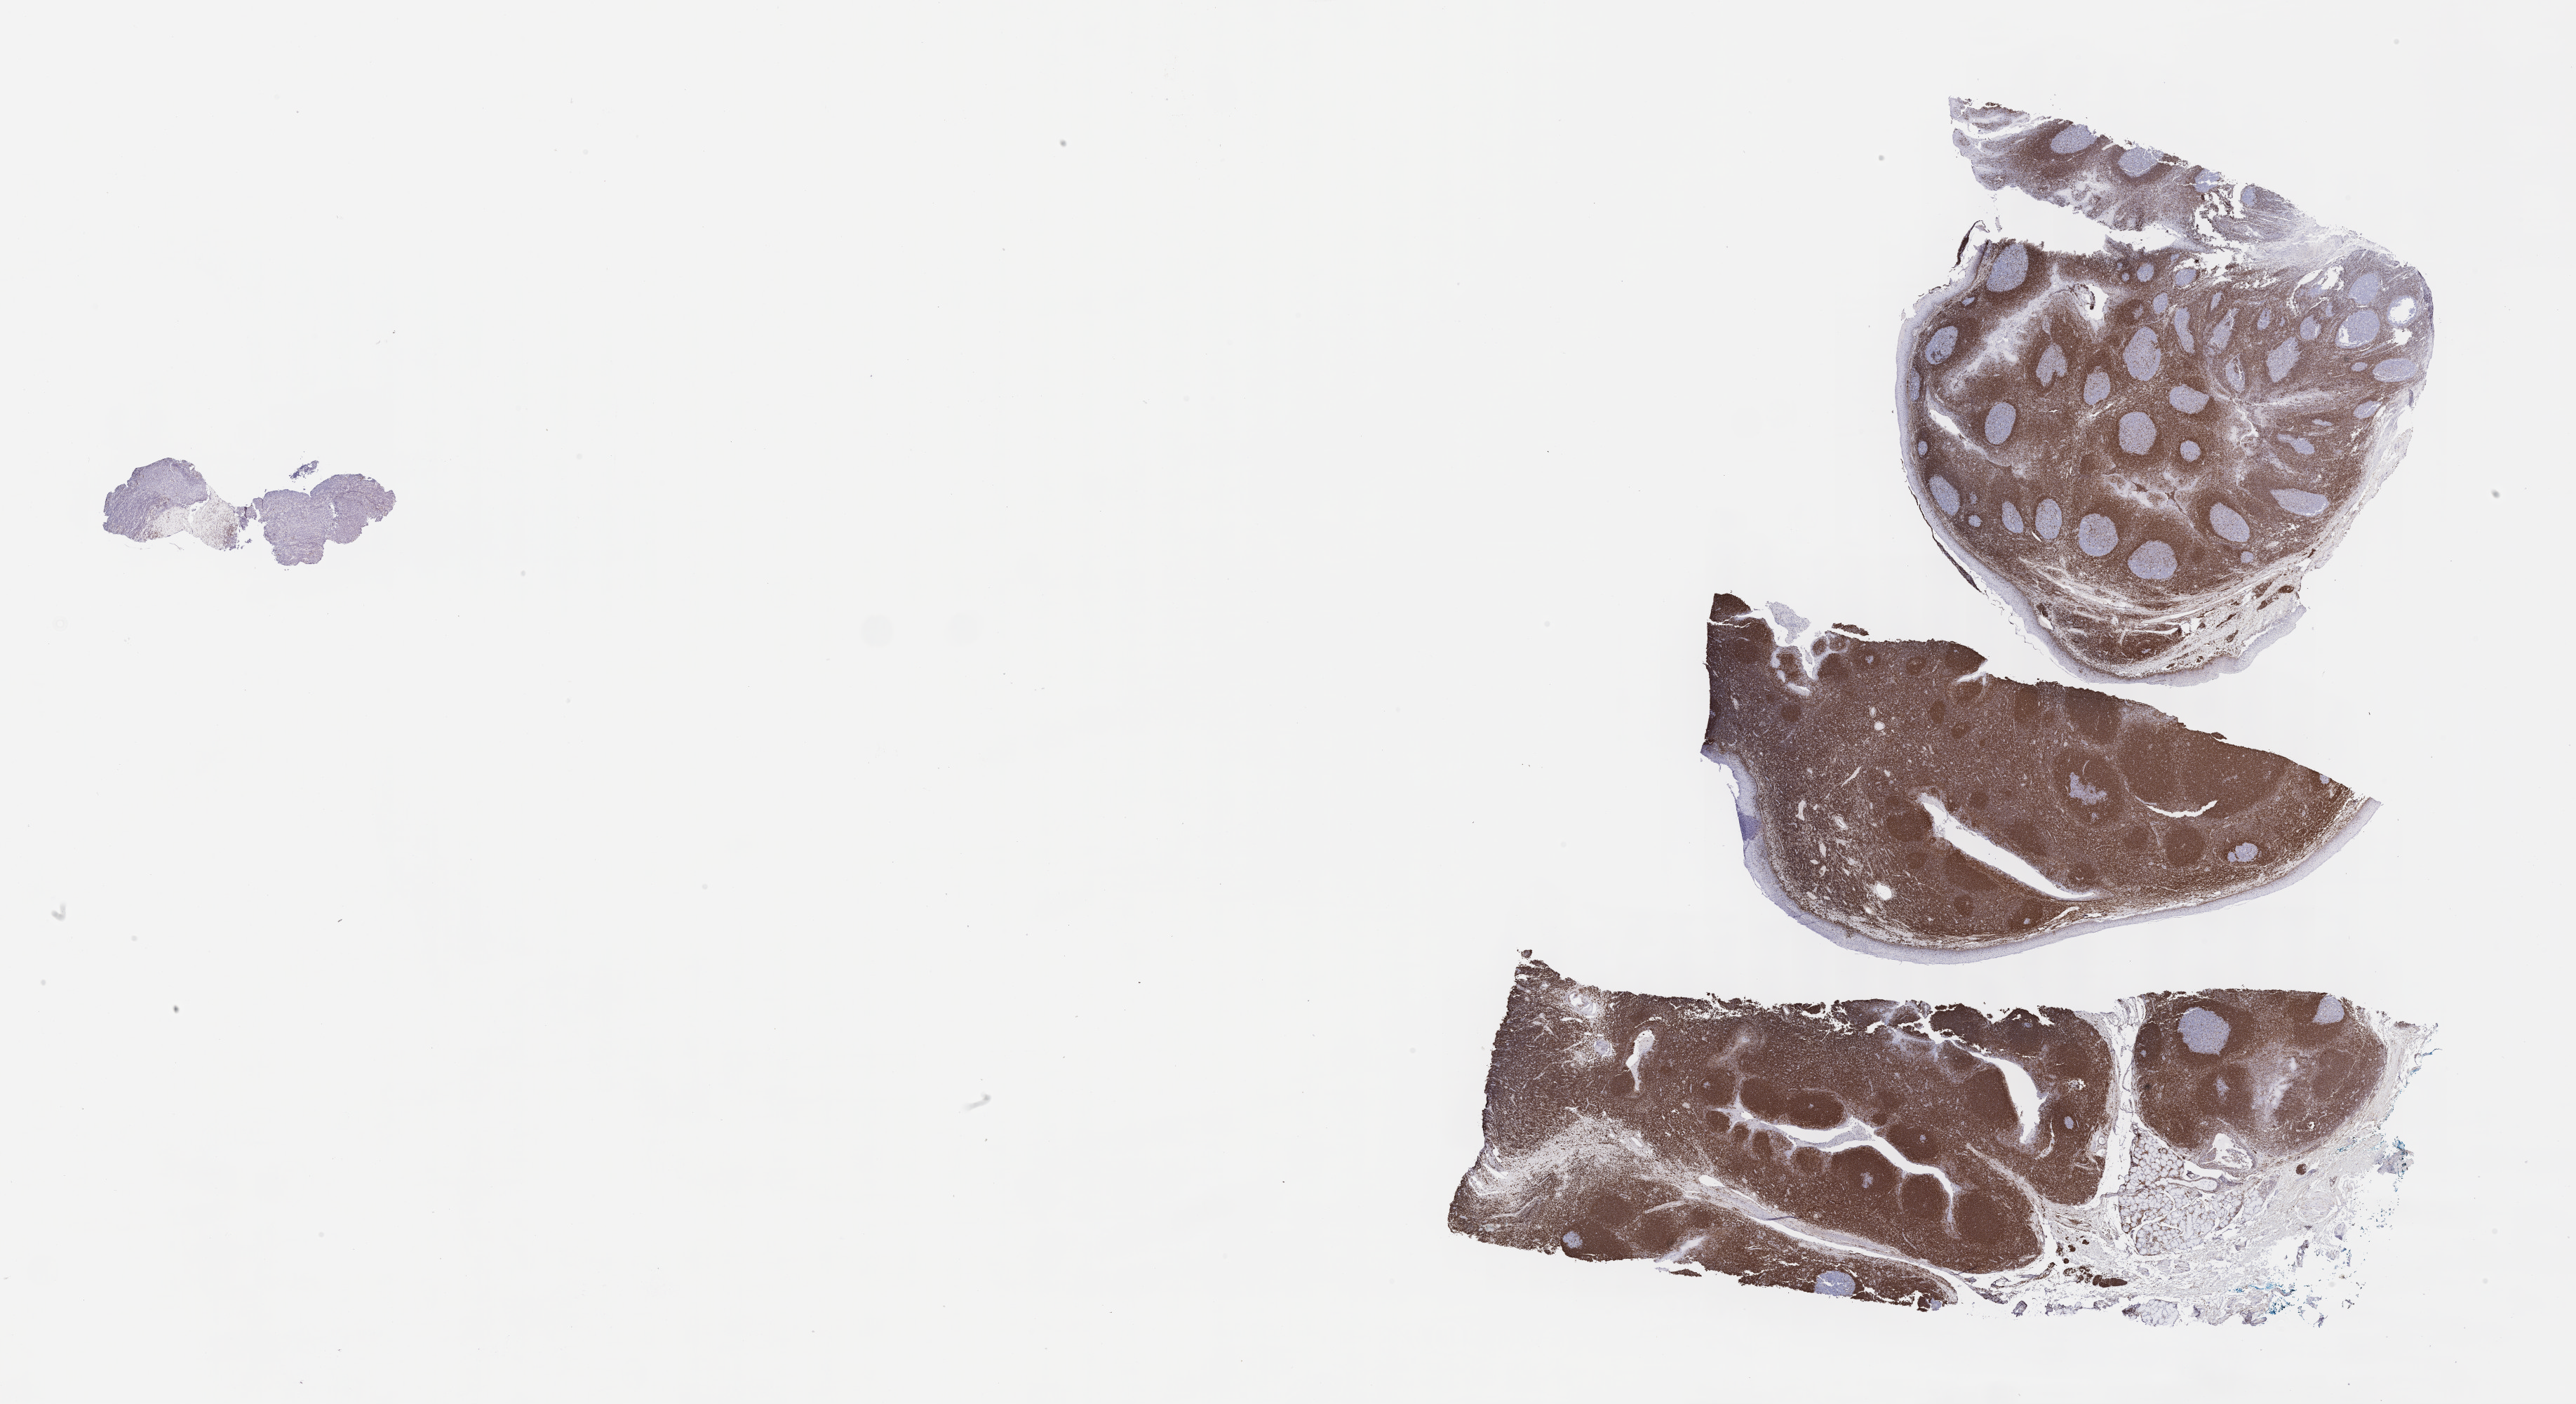
Whole-slide image, immunohistochemical stain for BCL2 — whole scanned area (about 29.7 x 16.2 mm) shown as a low-resolution overview; specimen: tumor tissue. Patient: male, aged 15.
Diagnosis: Burkitt lymphoma, NOS.